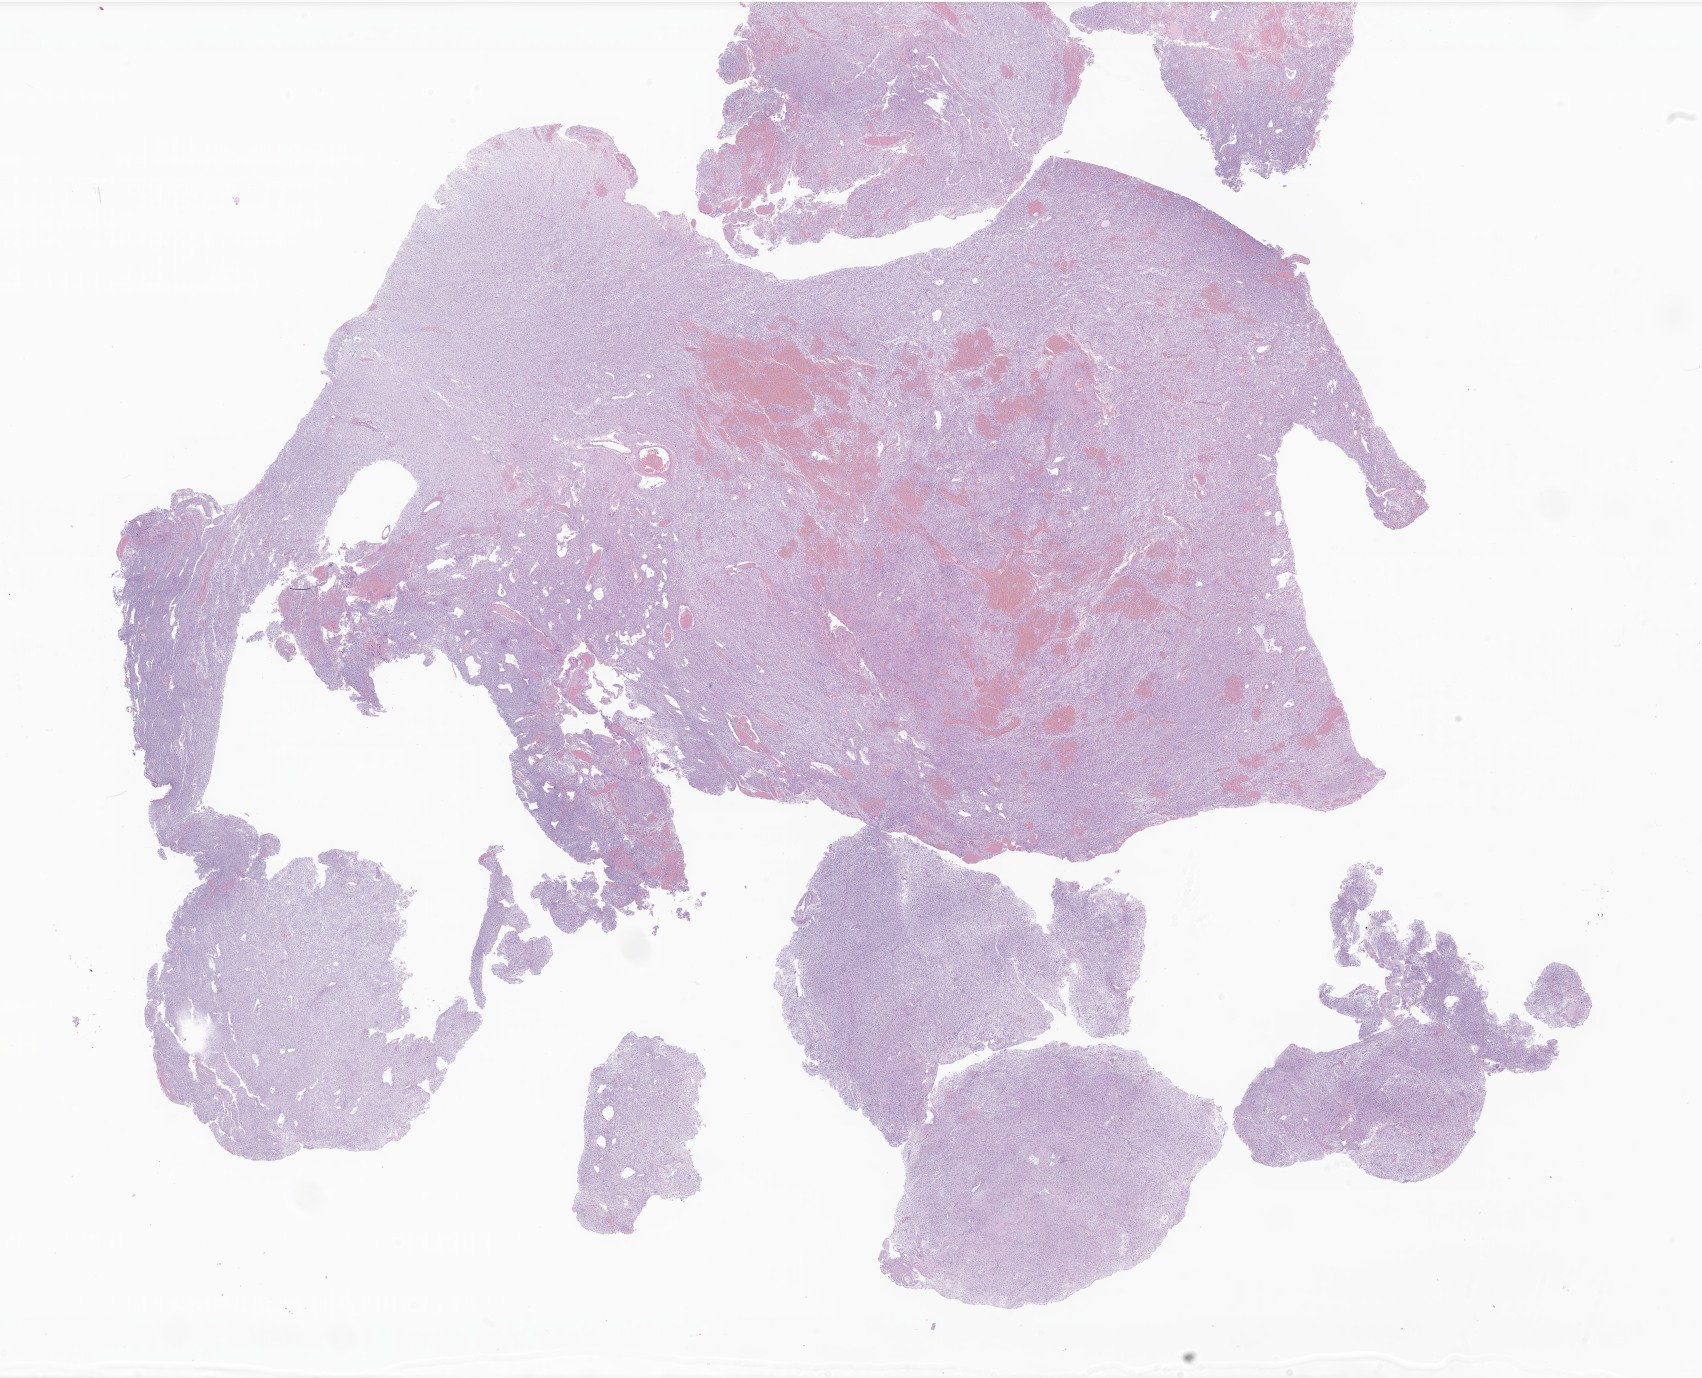
Whole-slide image, hematoxylin and eosin (H&E) stain of tumor tissue from the brain — low-resolution overview of the scanned area, about 28.7 x 23.2 mm. Formalin-fixed paraffin-embedded section. Female patient, age 156 months (13 years).
- diagnosis: Glioma, malignant